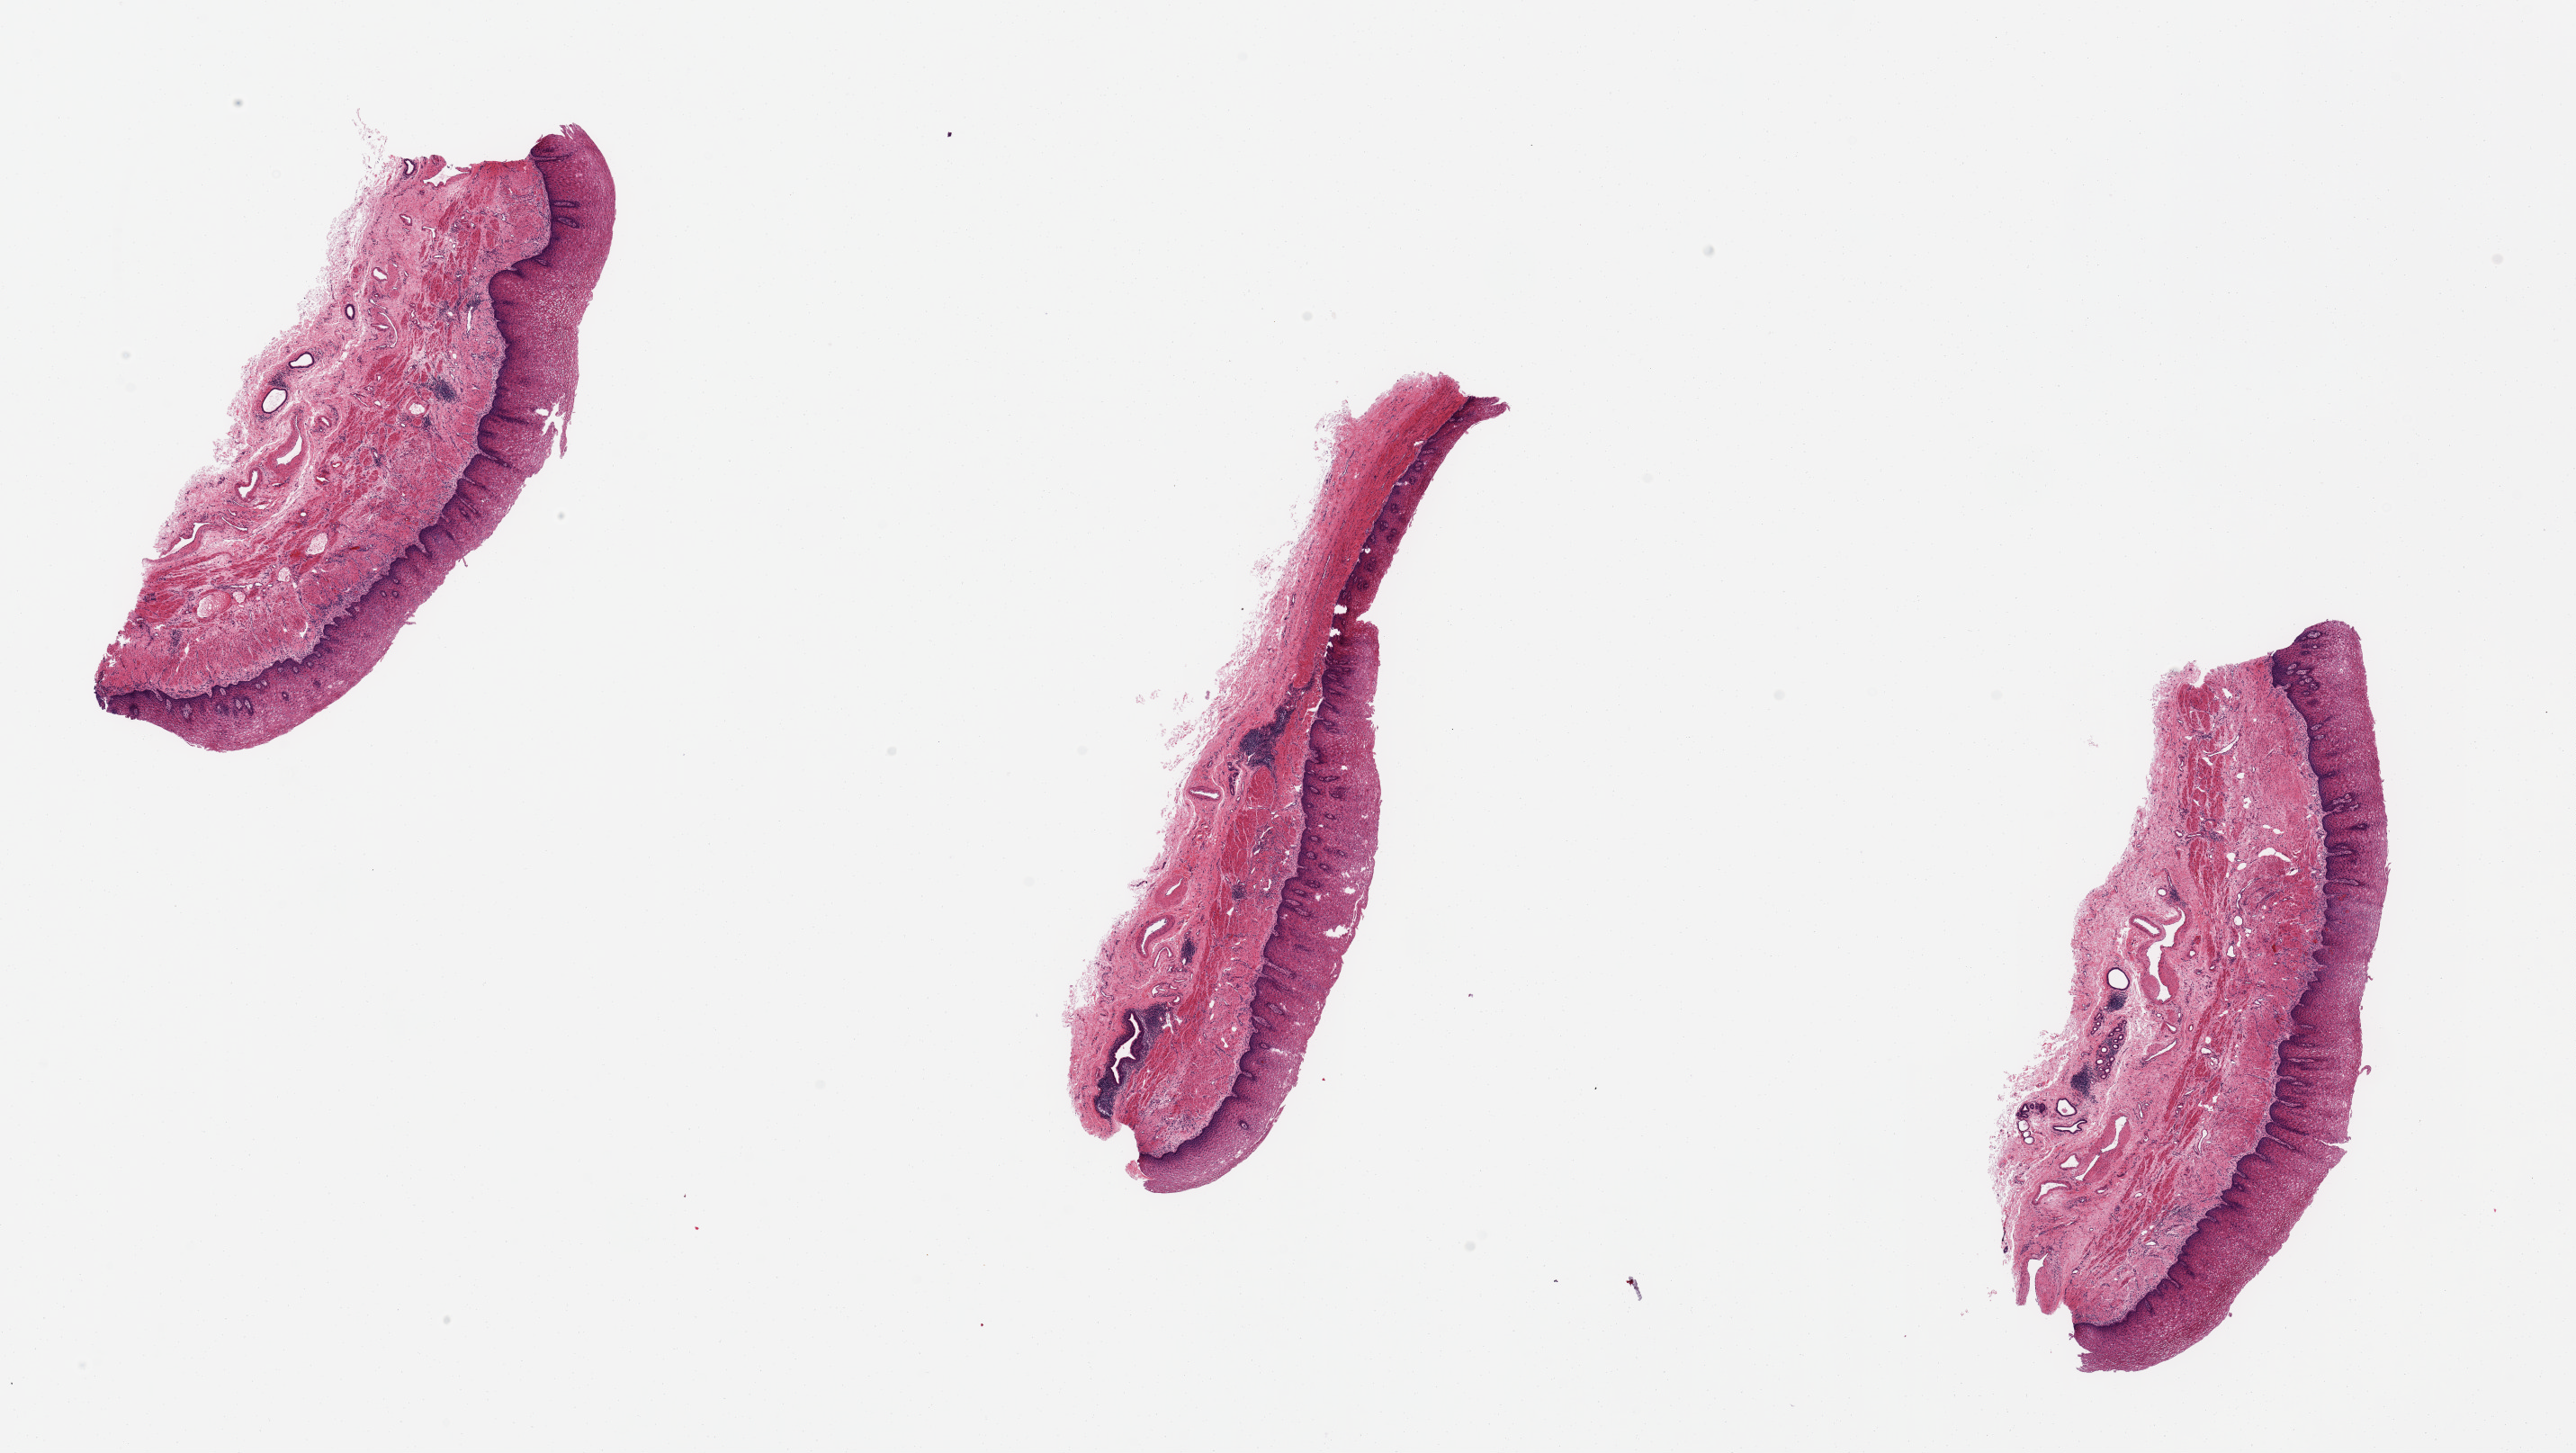
H&E whole-slide image — shown as a low-resolution overview of the whole scanned area (about 22.6 x 12.8 mm, acquisition: 20x scan), PAXgene-fixed paraffin-embedded (PFPE) section, target tissue: esophageal mucous membrane, donor tissue sample. Donor sex: female.
Reviewer comment on this tissue sample: 3 ~6x2mm pieces. Squamous mucosa is 20-25% of thickness.